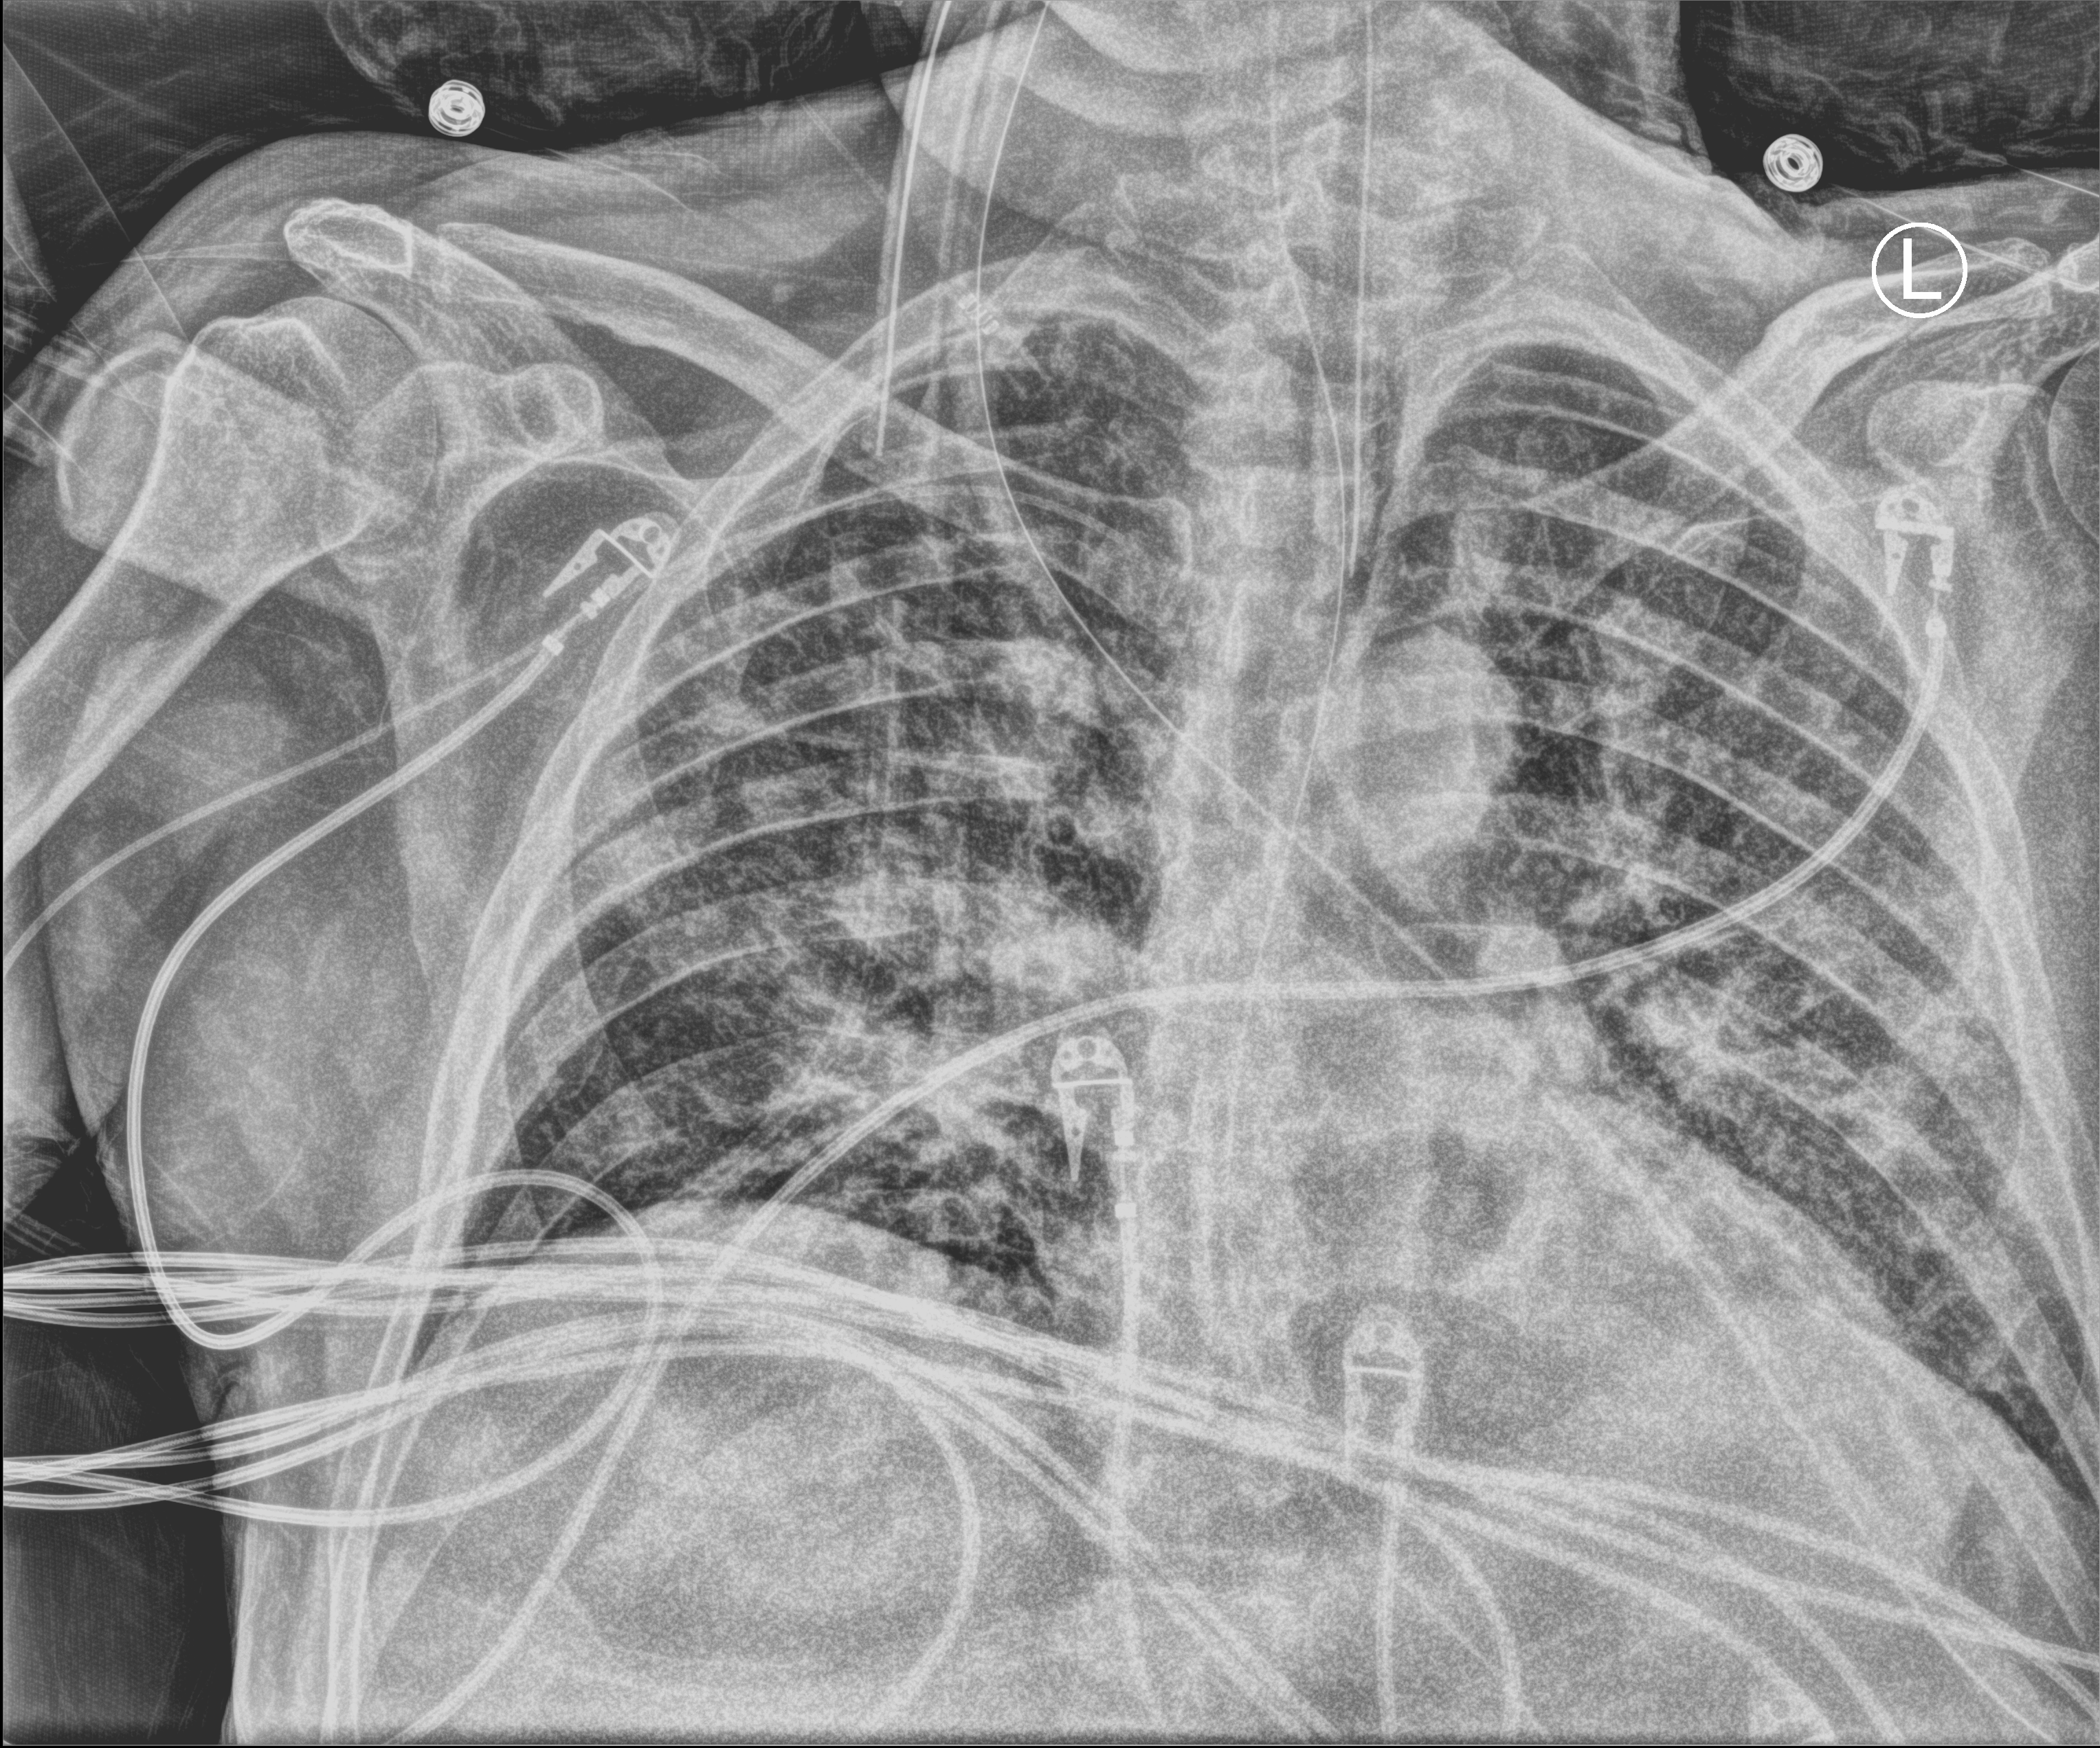
Portable chest radiograph. Male patient hospitalised with COVID-19, age 60–74 years.
Hospital-stay facts (about this admission, not read from this image; timing relative to this image not recorded): smoking status (admission record): never; hypertension (admission record): no; admitted to intensive care during this hospital stay: yes.